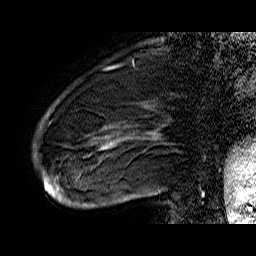
Breast MRI (dynamic contrast-enhanced), one sagittal slice. Position 12 of 60 along the scan axis. Dynamic contrast-enhanced series, time point 2 of 6 at this slice position (early post-contrast). 1.5 T. TE 6.4 ms, TR 32.9 ms. 4 mm slice thickness. 256 × 256 image matrix, field of view 200 × 200 mm. Female patient. Case-level facts recorded for this patient, not image findings: setting: breast cancer imaged before/during neoadjuvant chemotherapy; receptor status: HR-positive, HER2-negative.
Outlined on this slice (semi-automatically segmented with operator editing):
- analysis volume of interest (the breast-tissue region the enhancement analysis was run in; not a lesion): bounding box <43,74,176,208> (left, top, right, bottom; pixels)
- tumour enhancement mask (voxels above the 100 % enhancement threshold inside the analysis volume of interest): <43,114,124,202>